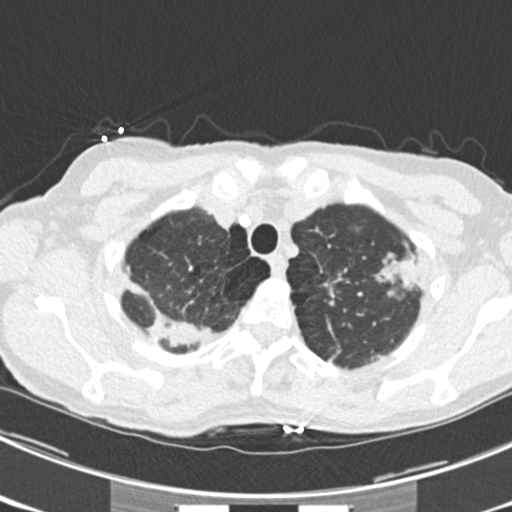
Axial slice from a low-dose chest CT screening exam; third annual screen; lung window (W 1500 / L -600 HU); standard (soft-tissue) reconstruction kernel (B30f); 120 kVp; slice 39 of 225 in the series. Female participant, aged 63 years at enrolment. Current smoker at enrolment.
- Expert reader's lesion annotation, bounding box (x1, y1, x2, y2) in pixels: (372, 242, 438, 305).
- The screening reader recorded 9 non-calcified nodules or masses ≥4 mm on this exam (left upper lobe, right upper lobe, left upper lobe, left lower lobe, right middle lobe, left lower lobe, left lower lobe, right lower lobe, right lower lobe); which of them this box marks is not recorded.
- Official screen result: positive, other.